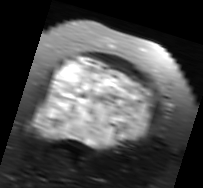
MRI of an extremity soft-tissue mass, one axial slice; position 50 of 91 along the scan axis; T2-weighted fat-saturated; MR volume resampled by the dataset authors to the PET/CT grid (not the native acquisition matrix); 3.27 mm slice thickness; 203 × 188 image matrix, field of view 198 × 184 mm. Female patient. Case-level facts recorded for this patient, not image findings: histological type: malignant solitary fibrous tumor; grade: intermediate; site of the primary tumour: right thigh.
Annotated regions visible in this slice (expert contour drawn on MRI and transferred to this co-registered scan by the dataset authors):
- gross tumour volume including surrounding oedema: bounding box <28,56,157,150> (left, top, right, bottom; pixels)
- gross tumour volume (mass): <33,56,153,148>